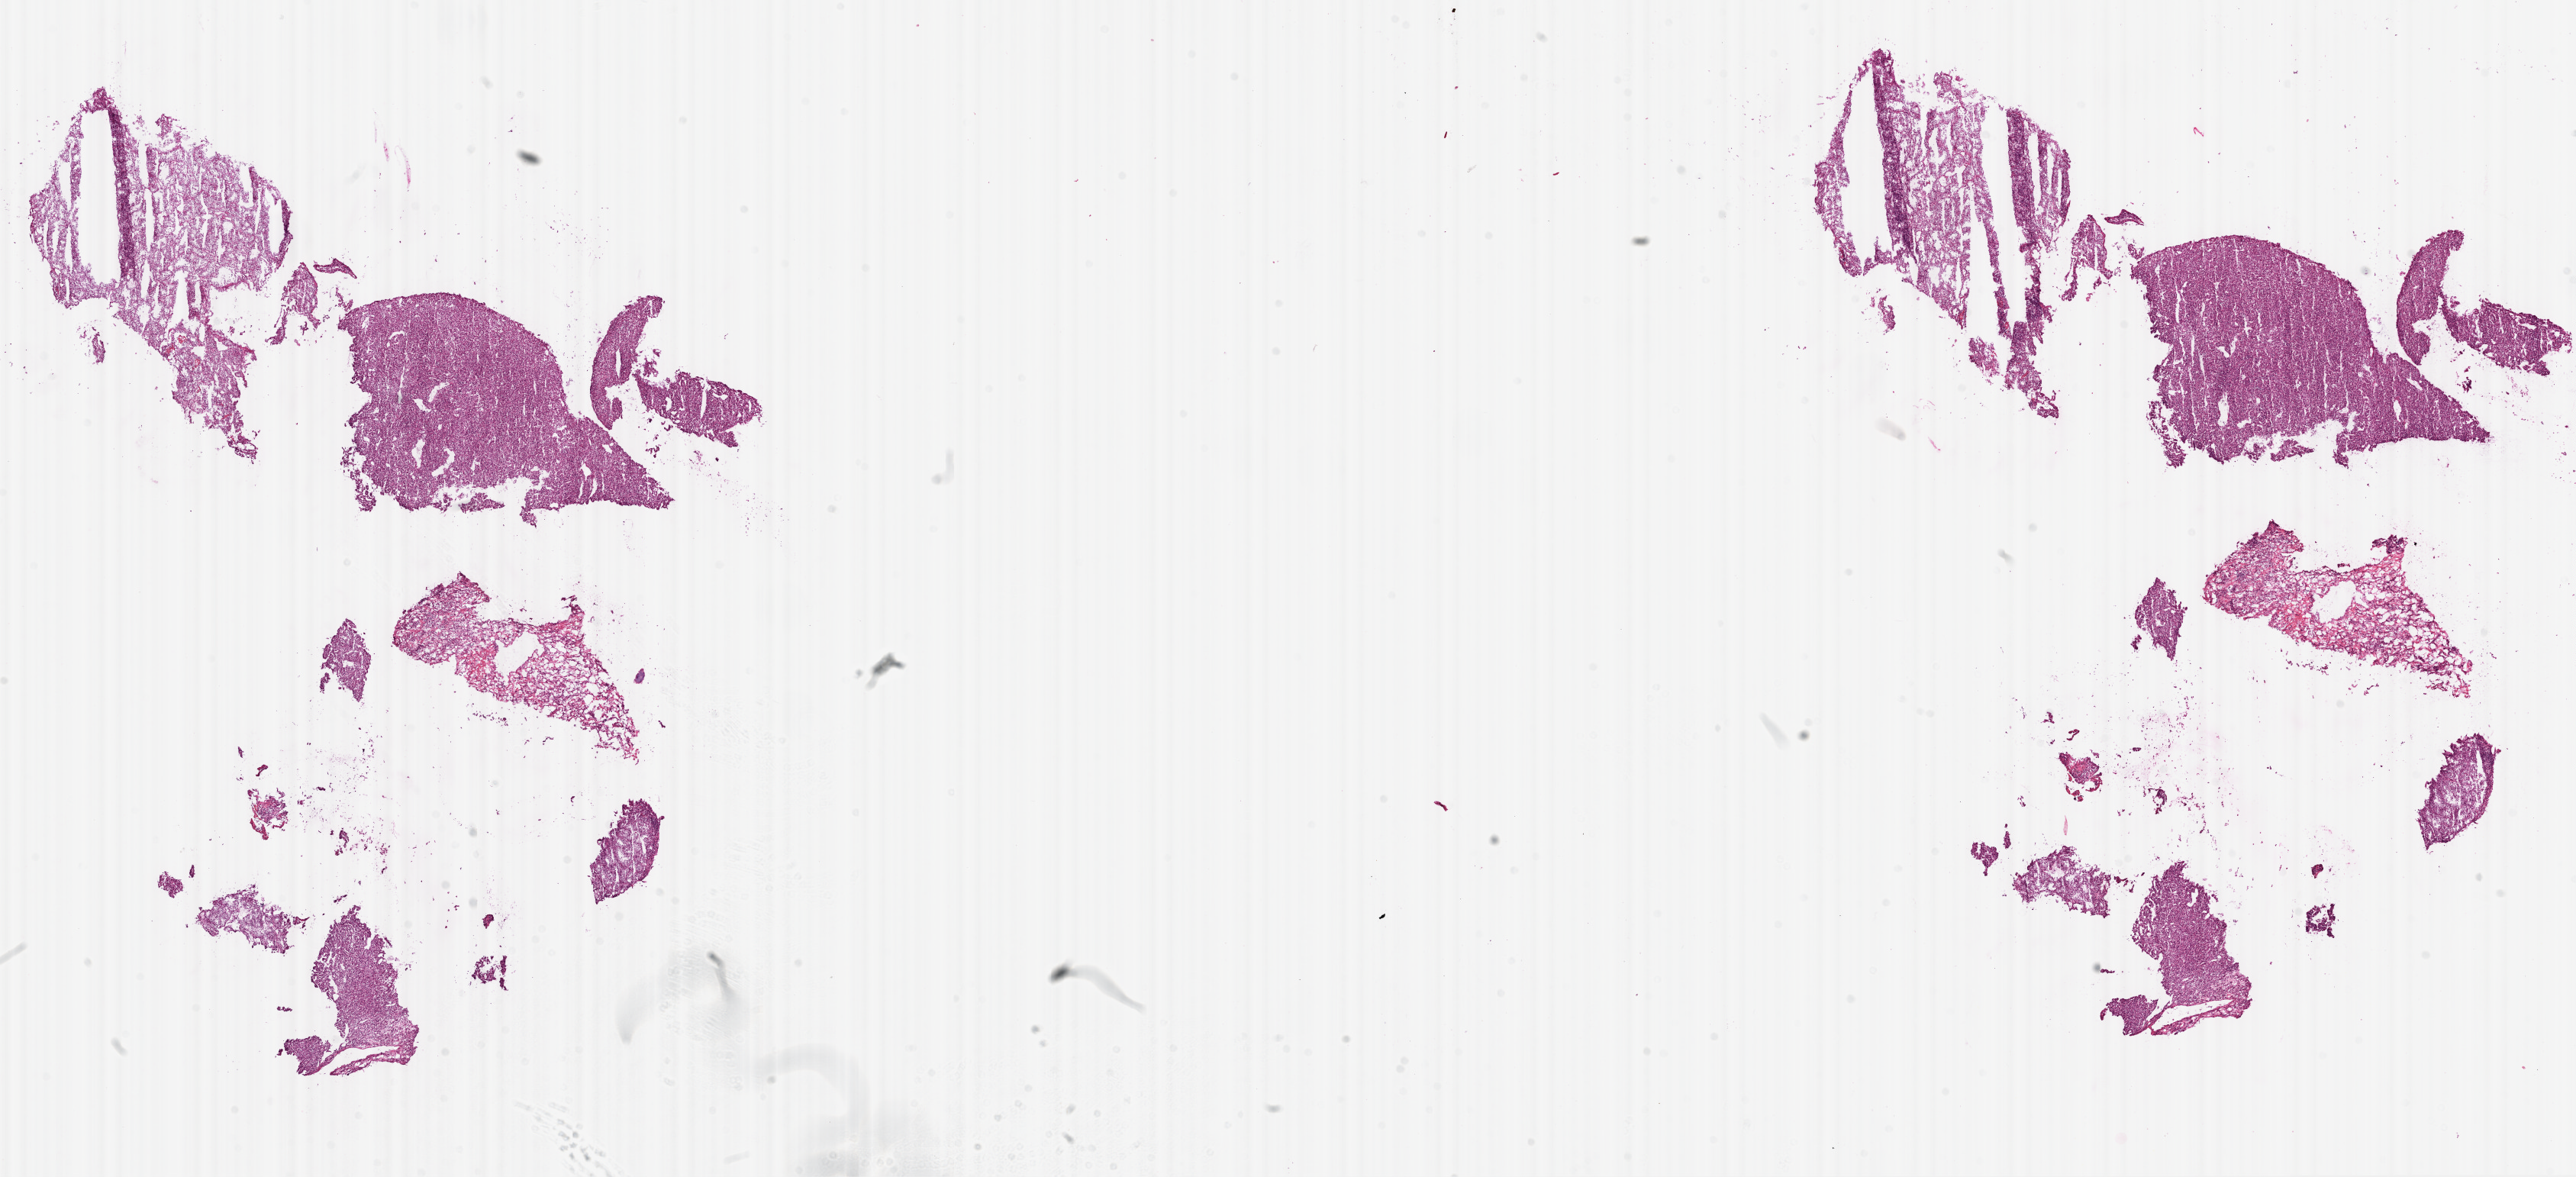
Digitized H&E-stained tissue section (whole slide) — a low-resolution overview of the entire scanned area, about 27.1 x 12.4 mm; frozen section from the top of the tissue portion; kidney, primary tumour sample. Female patient; age at initial diagnosis 67 years. Slide review estimates, as recorded: tumour cells 95%, tumour nuclei 85%.
Diagnosis: Clear cell adenocarcinoma, NOS.